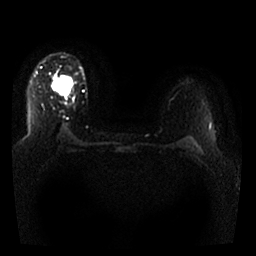
Breast MRI, one axial slice. Position 22 of 25 along the scan axis. Diffusion-weighted series; image 2 of 4 stored at this slice position (different b-values; order by instance number). 1.5 T. 4 mm slice thickness. 256 × 256 image matrix. Female patient.
Annotated regions visible in this slice (manually delineated by an expert):
- tumour on diffusion-weighted imaging: bounding box (x1, y1, x2, y2) in pixels: (52, 75, 74, 96)